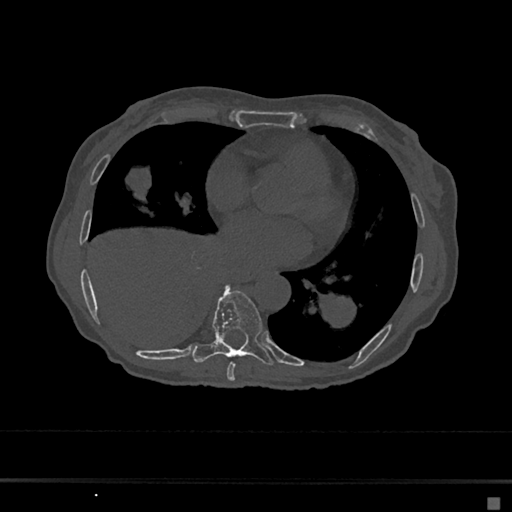
CT including the spine, one axial slice. Position 331 of 797 along the scan axis. Reconstruction kernel Br40s/3. 120 kVp. Bone window (W 1800 / L 400 HU). 0.5 mm slice thickness. 512 × 512 image matrix, field of view 360 × 360 mm. Patient: female, 68 years. From the clinical record (not read from this slice): primary cancer: renal.
Outlined on this slice (semi-automatically segmented with operator editing):
- T7 vertebra: bounding box [x1, y1, x2, y2] px = [227, 362, 235, 381]
- T8 vertebra: [192, 285, 273, 365]